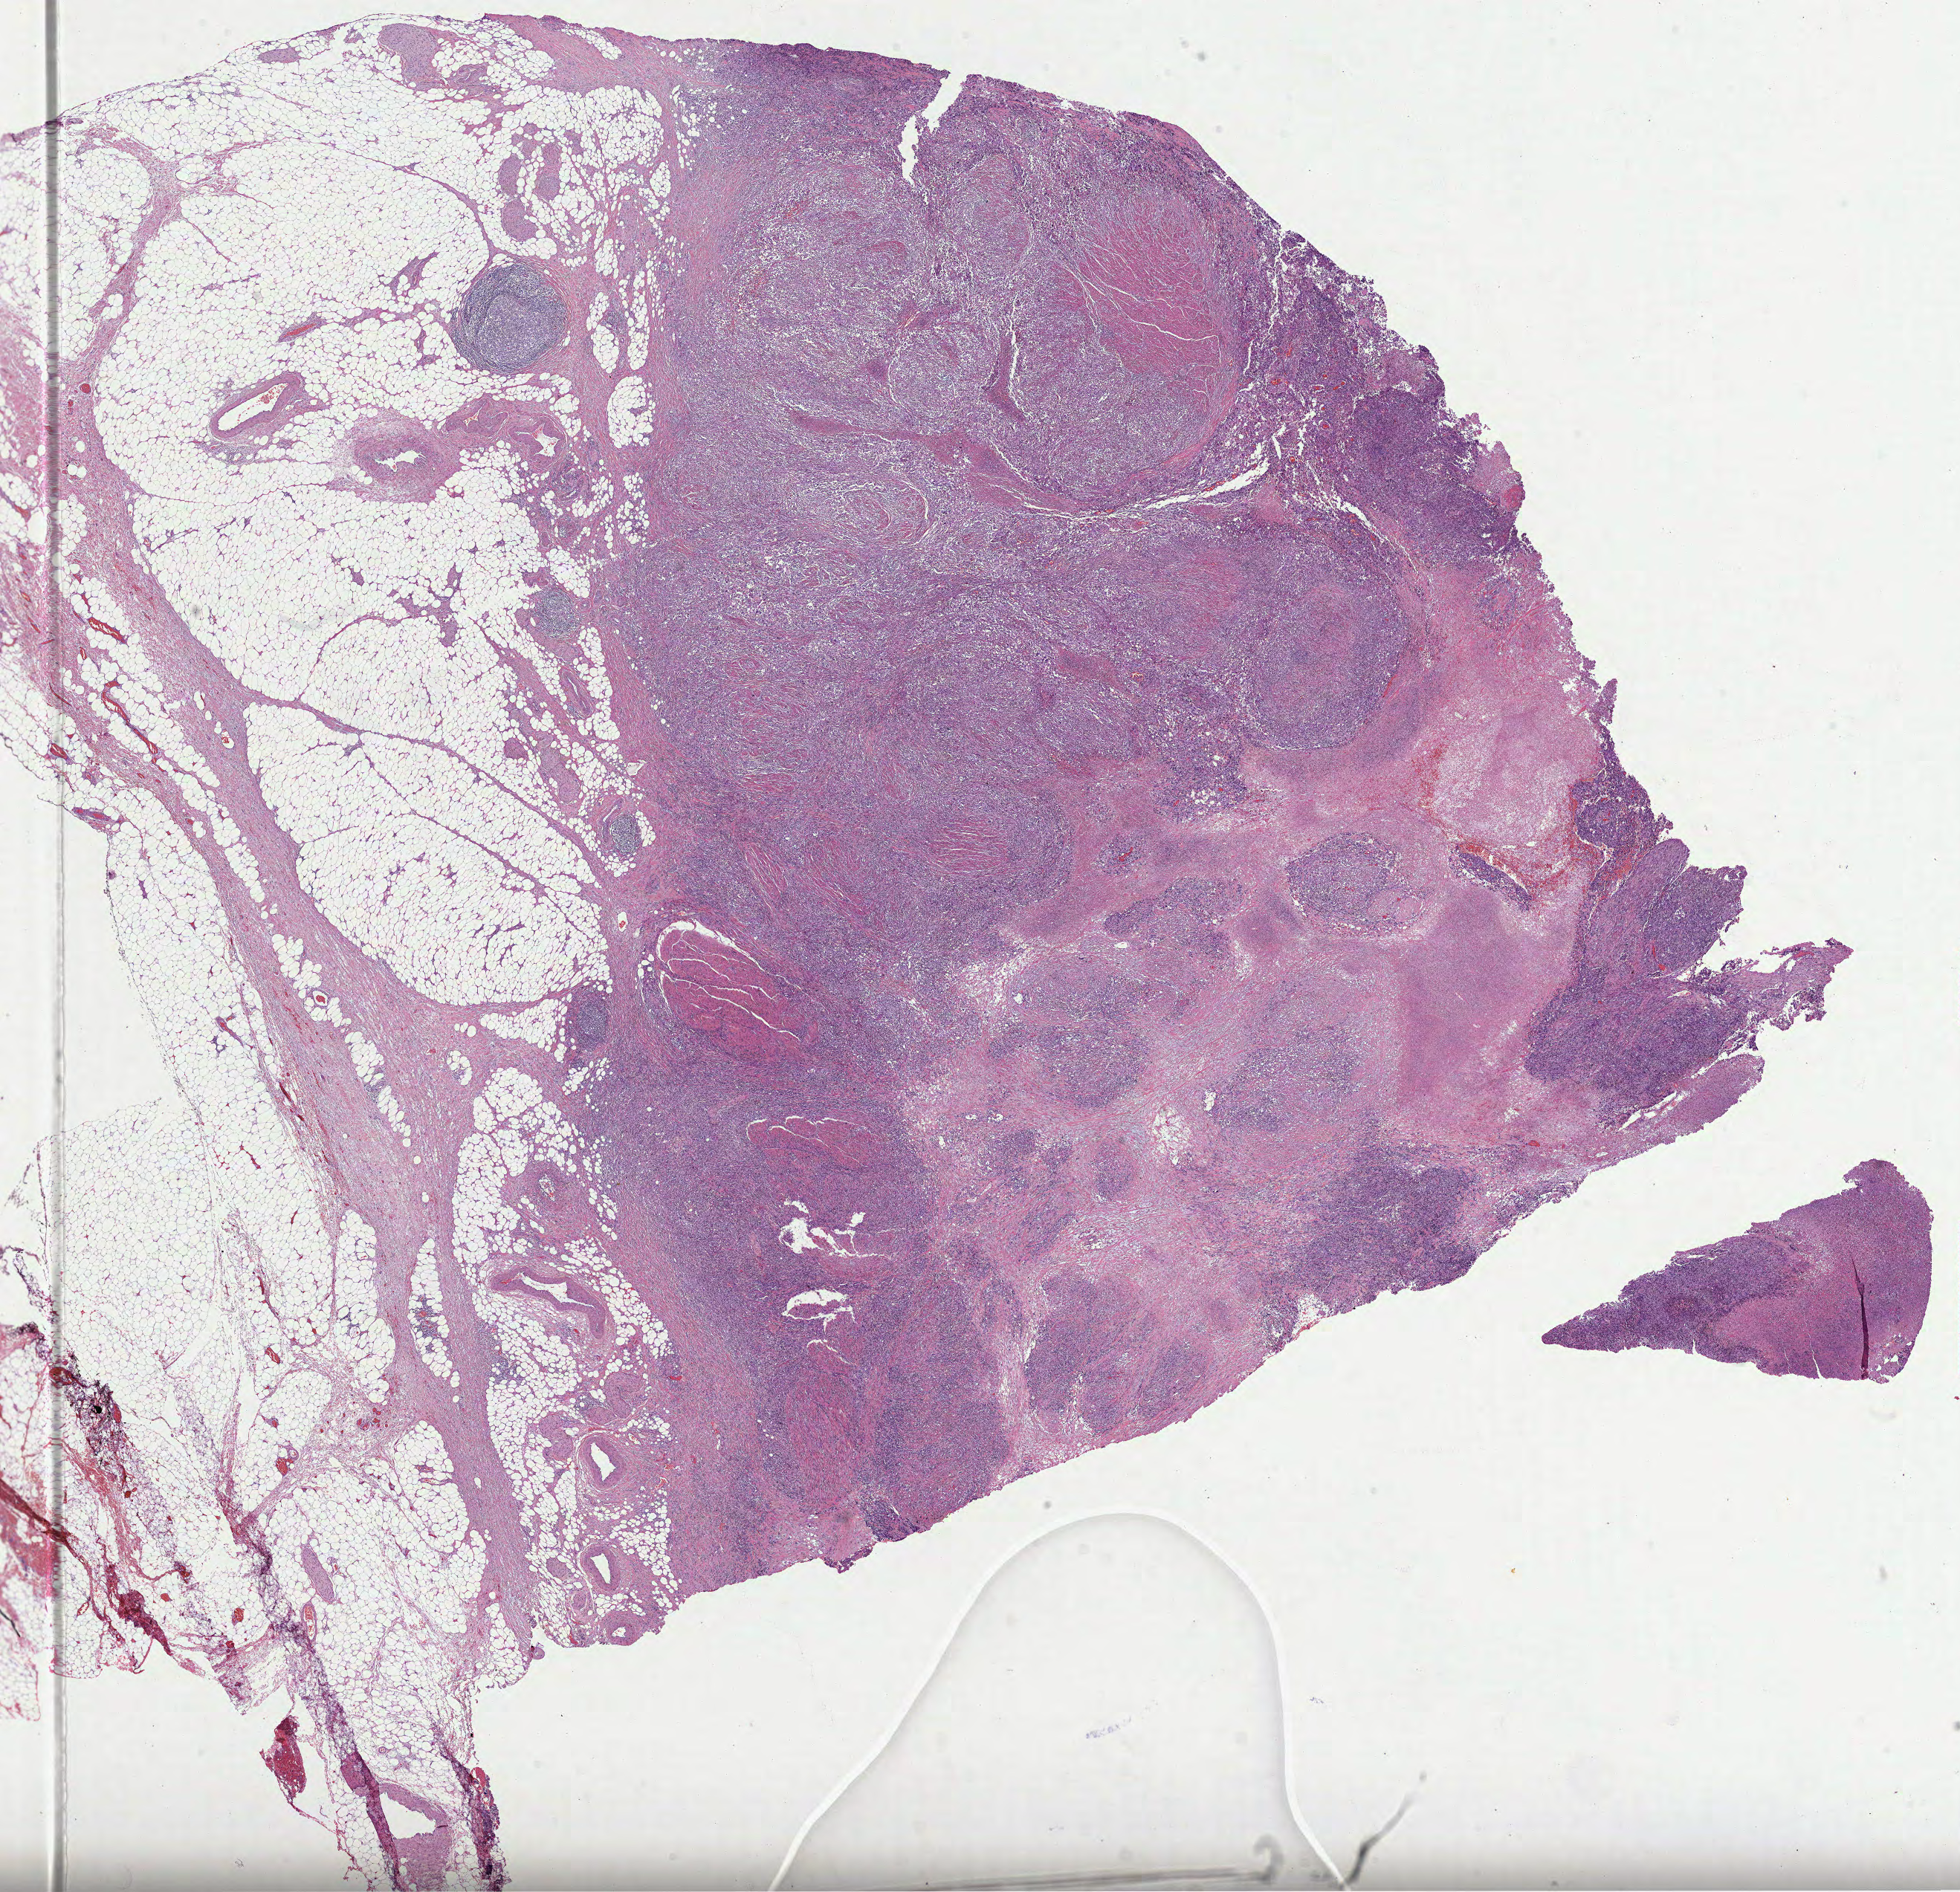
Digitized Hematoxylin and eosin (H&E) stained tissue section (whole slide) — whole scanned area (about 21.3 x 20.5 mm, slide scanned at 40x) shown as a low-resolution overview. Formalin-fixed paraffin-embedded (FFPE) diagnostic section. Primary tumour sample from the bladder. Patient: male, age at initial diagnosis 71 years. Histologic grade: high grade.
TNM: T3a N0 M0. AJCC pathologic stage: III. Pathologic diagnosis: Transitional cell carcinoma.